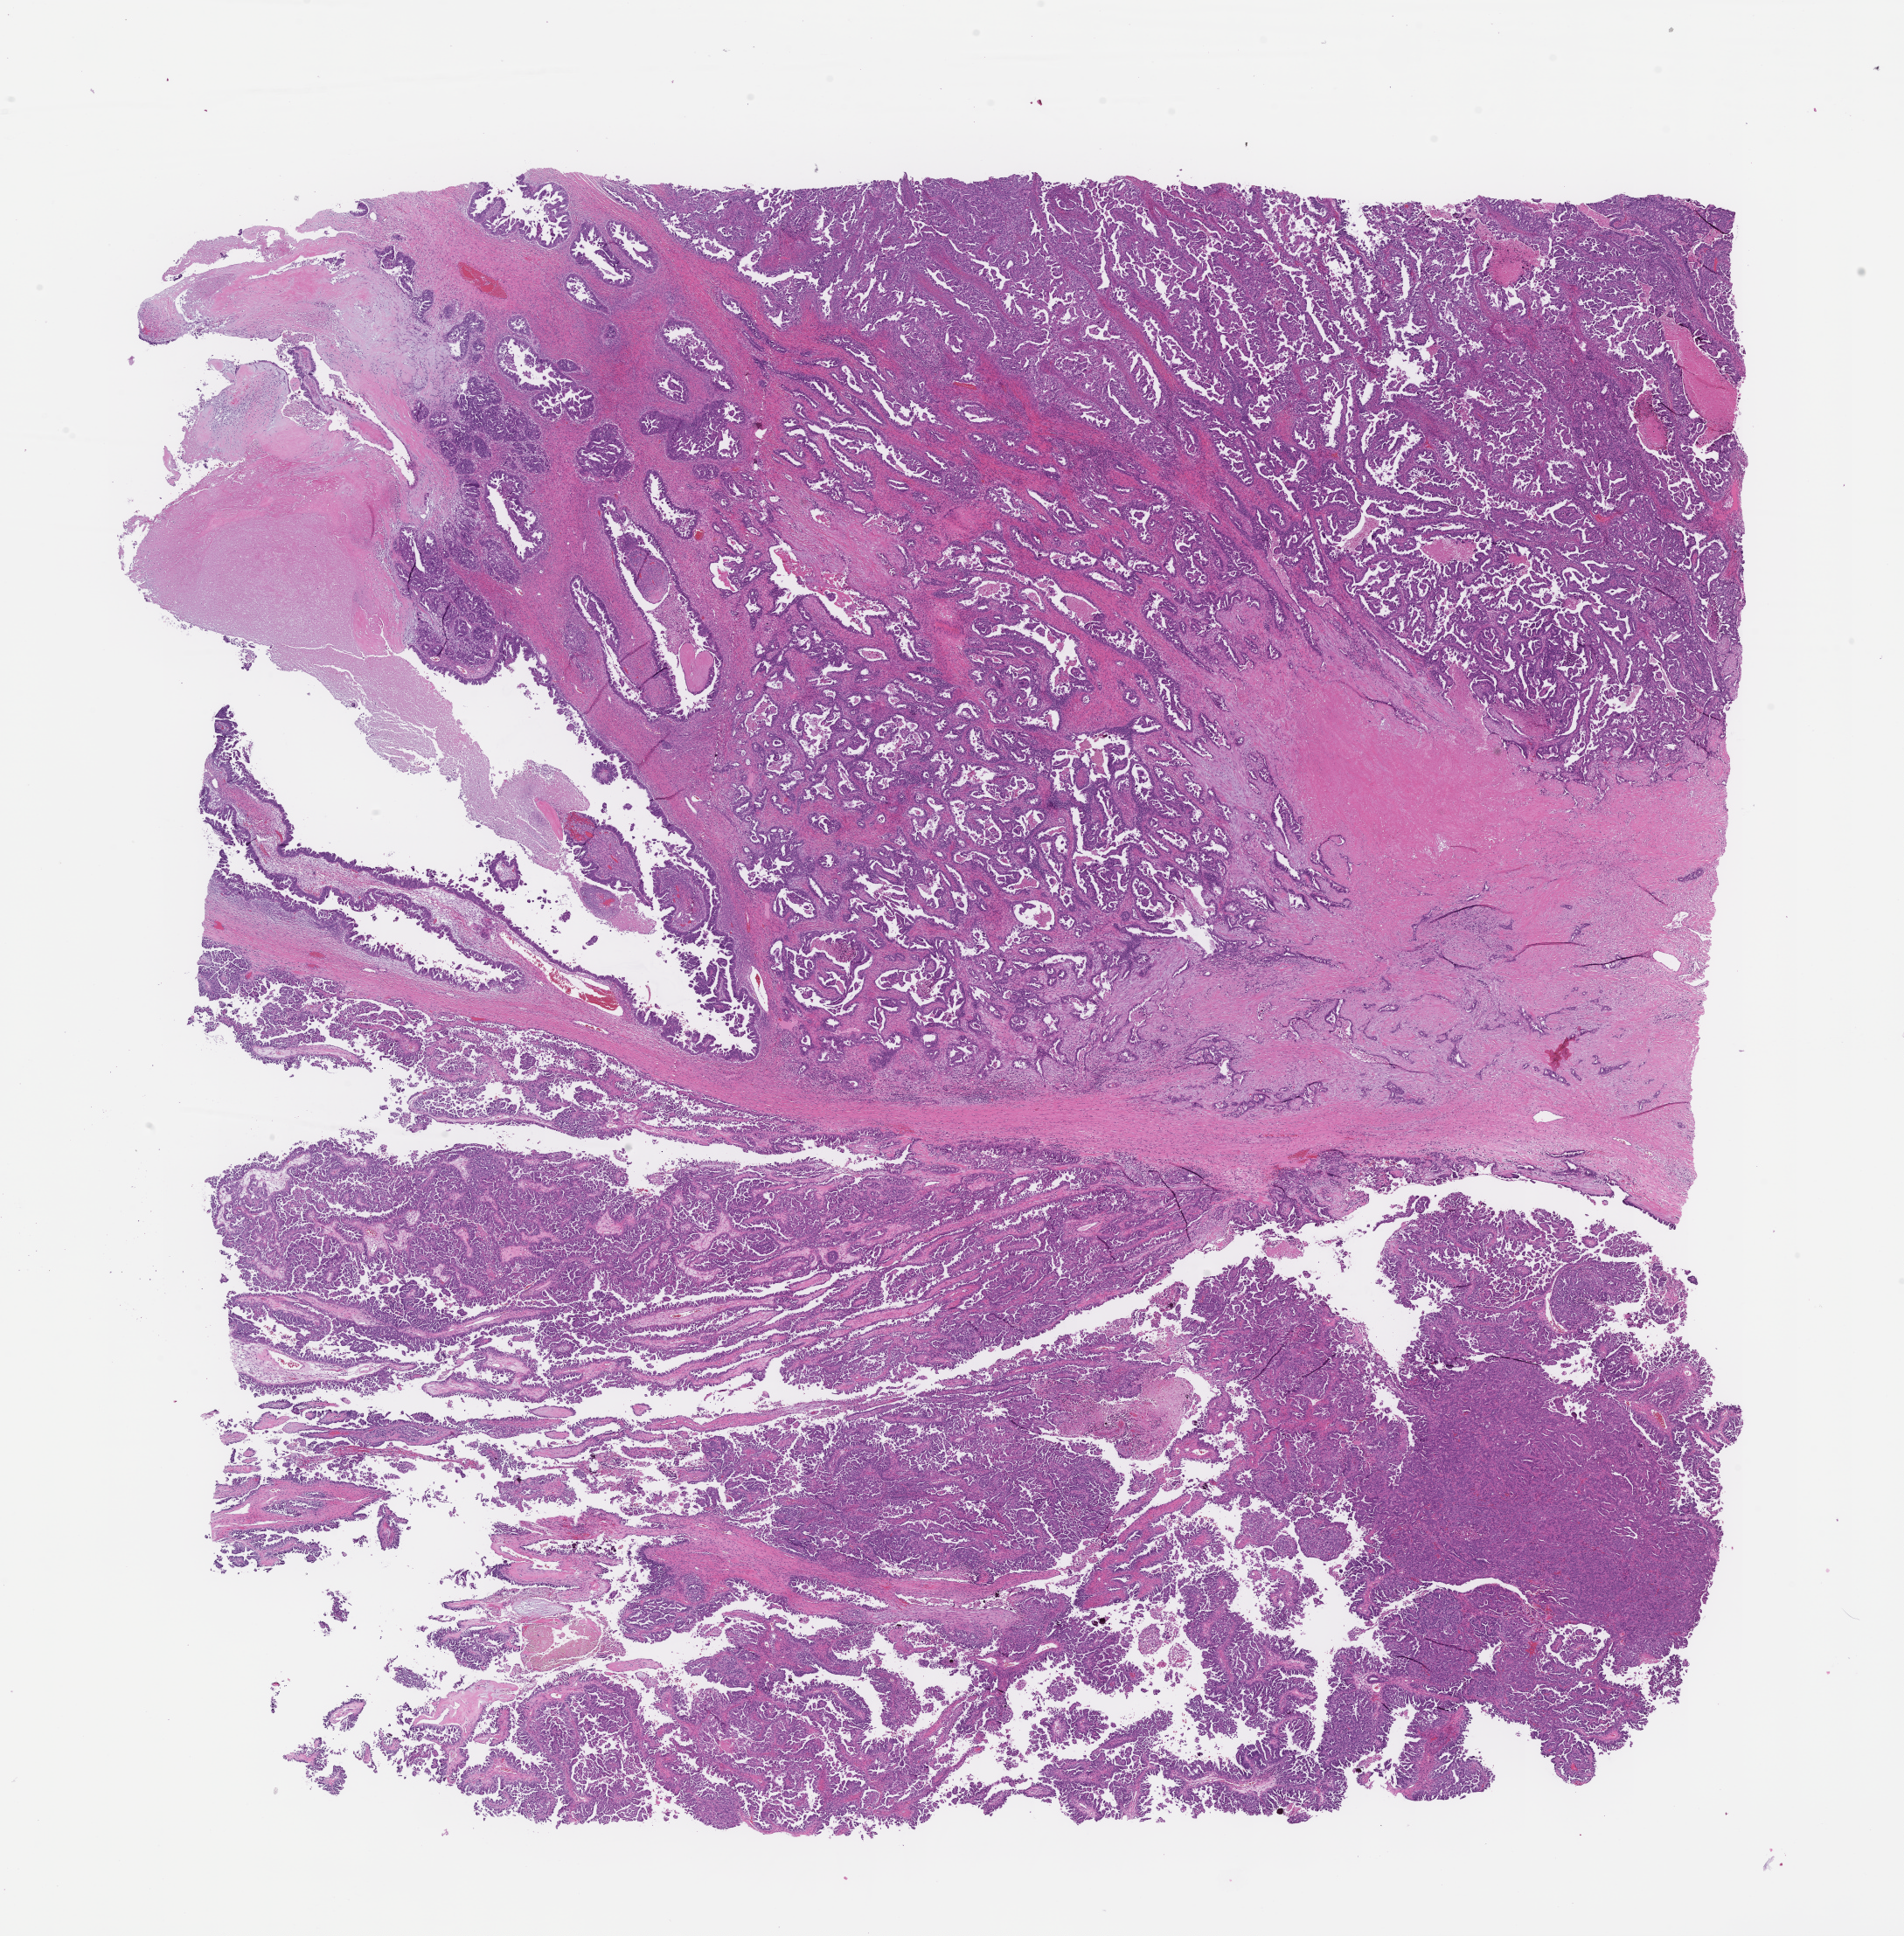
Whole-slide image, haematoxylin and eosin stain — whole scanned area (about 17.6 x 17.9 mm) shown as a low-resolution overview. FFPE section. Tissue site: ovary. Archival tissue. Patient: female.
* this section: primary tumor
* diagnosis: Ovarian Carcinoma